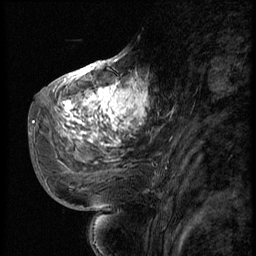
Breast MRI (dynamic contrast-enhanced), one sagittal slice; slice 28 of 56 in the series (ordered by position); 3 images stored at this slice position (order not interpretable as contrast timing); 1.5 T; TE 4.2 ms, TR 9 ms; 256 × 256 image matrix, field of view 180 × 180 mm. Patient: female, 51 years. Case-level facts recorded for this patient, not image findings: setting: breast cancer imaged before/during neoadjuvant chemotherapy; receptor status: triple-negative.
Outlined on this slice (semi-automatic segmentation, software-assisted and operator-edited):
- analysis volume of interest (the breast-tissue region the enhancement analysis was run in; not a lesion): bounding box <52,66,150,179> (left, top, right, bottom; pixels)
- tumour enhancement mask (voxels above the 140 % enhancement threshold inside the analysis volume of interest): <62,70,149,143>